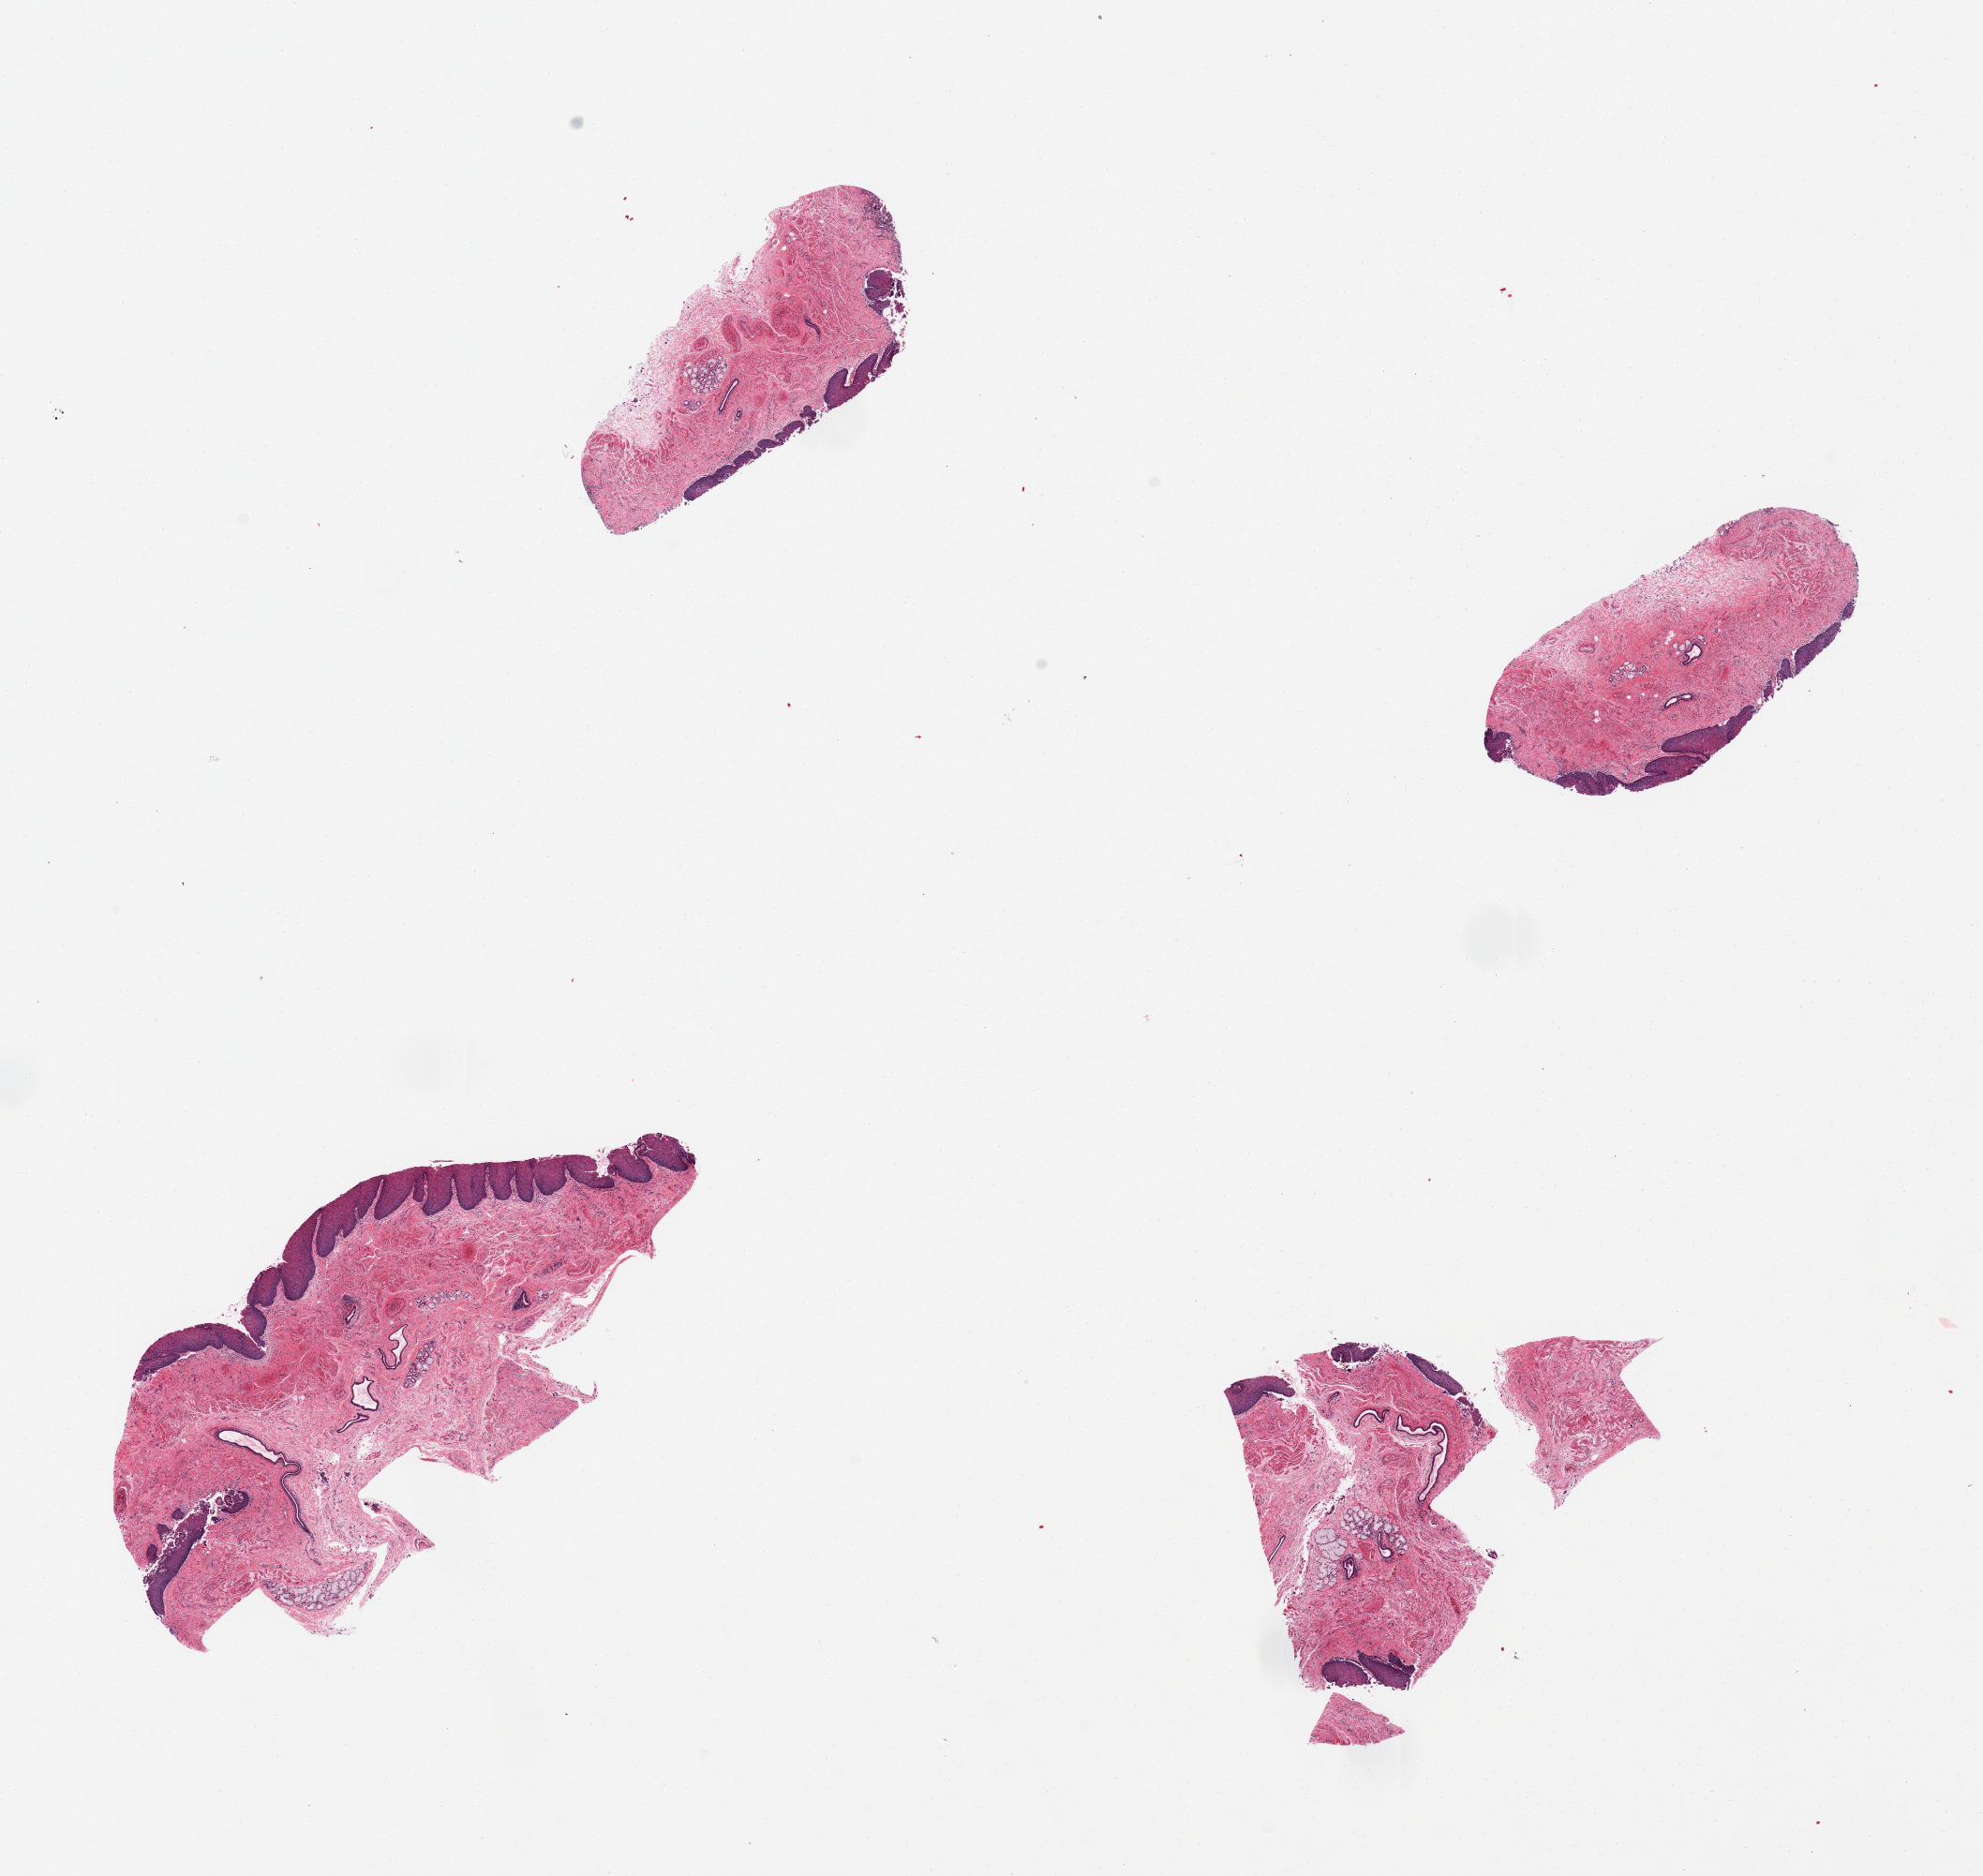
Whole-slide image, hematoxylin and eosin (H&E) stain, low-resolution overview of the scanned area, about 16.7 x 15.8 mm; PAXgene-fixed paraffin-embedded (PFPE) section; section of esophageal mucous membrane (target tissue); tissue donor sample. Donor sex: female.
Pathologist's review note for this sample: 4 pieces; partly sloughed epithelium; small samples.